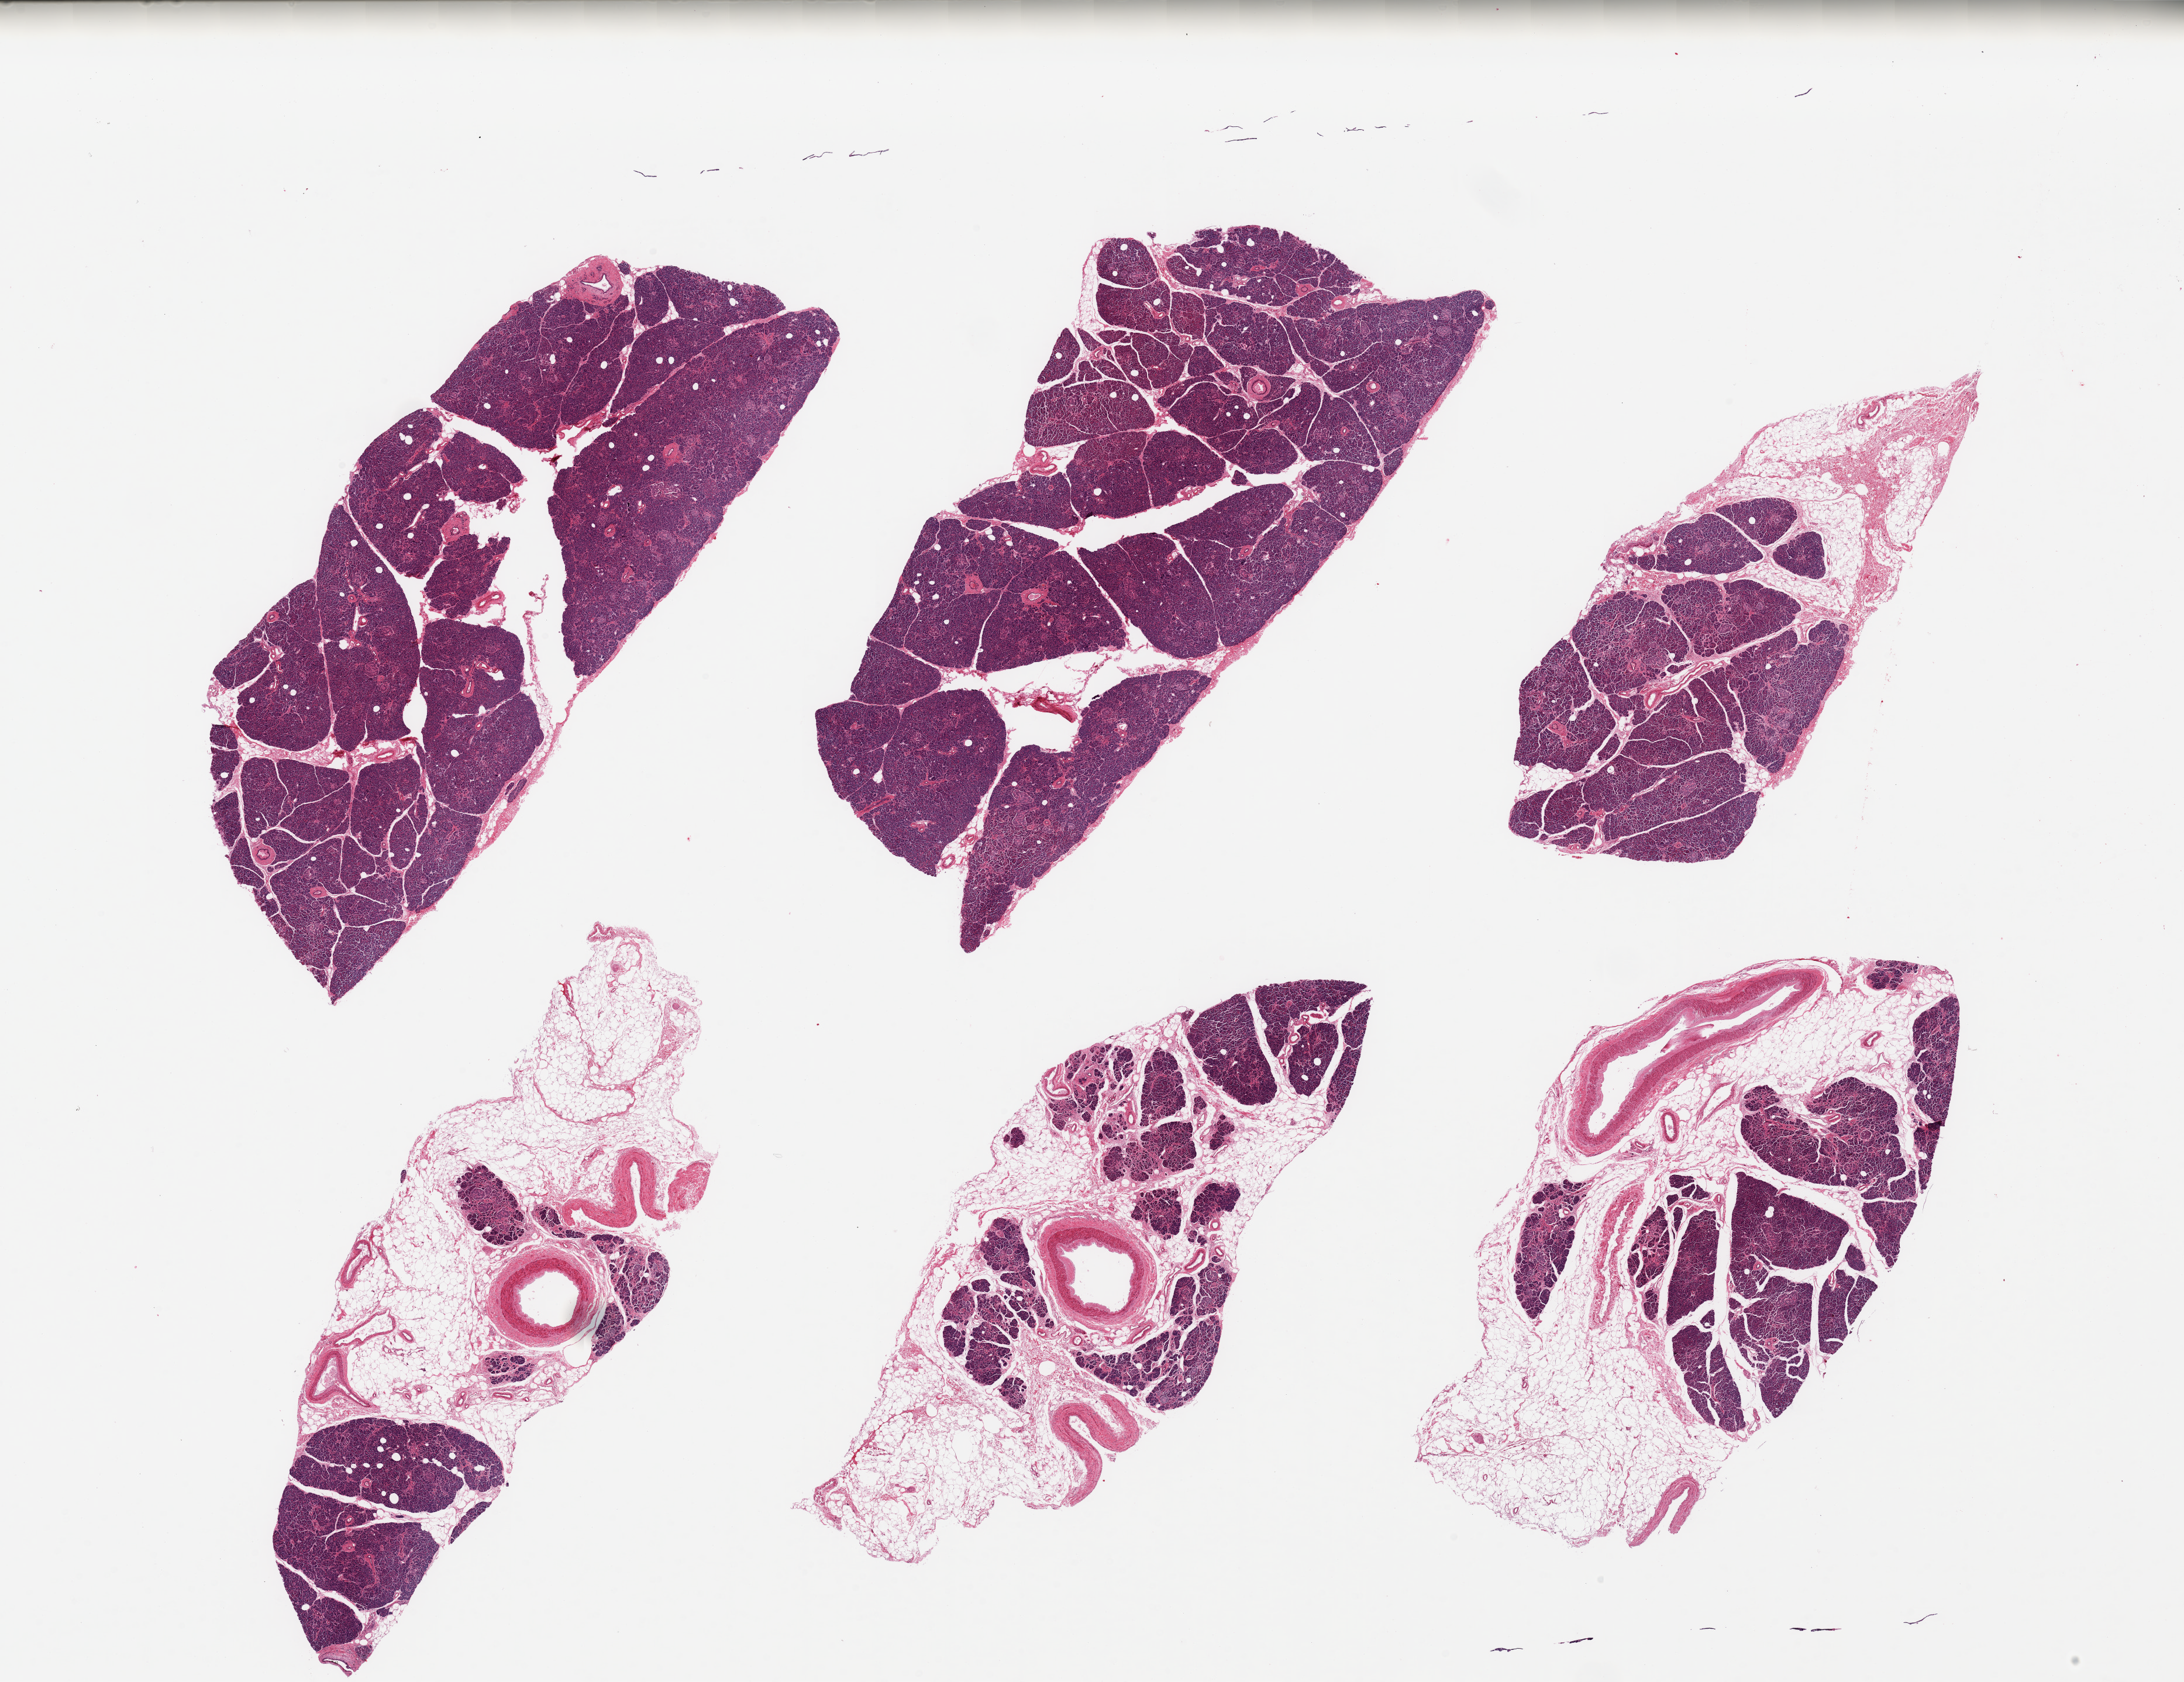
Whole-slide image, haematoxylin and eosin stain, shown as a low-resolution overview of the whole scanned area (about 29.5 x 22.7 mm). PAXgene-fixed, paraffin-embedded tissue. Target tissue: pancreas. Tissue donor sample.
* review note (as recorded): 6 pieces; well preserved pancreas with accentuation of Langerhans cells; 10% to 60% internal/external fat